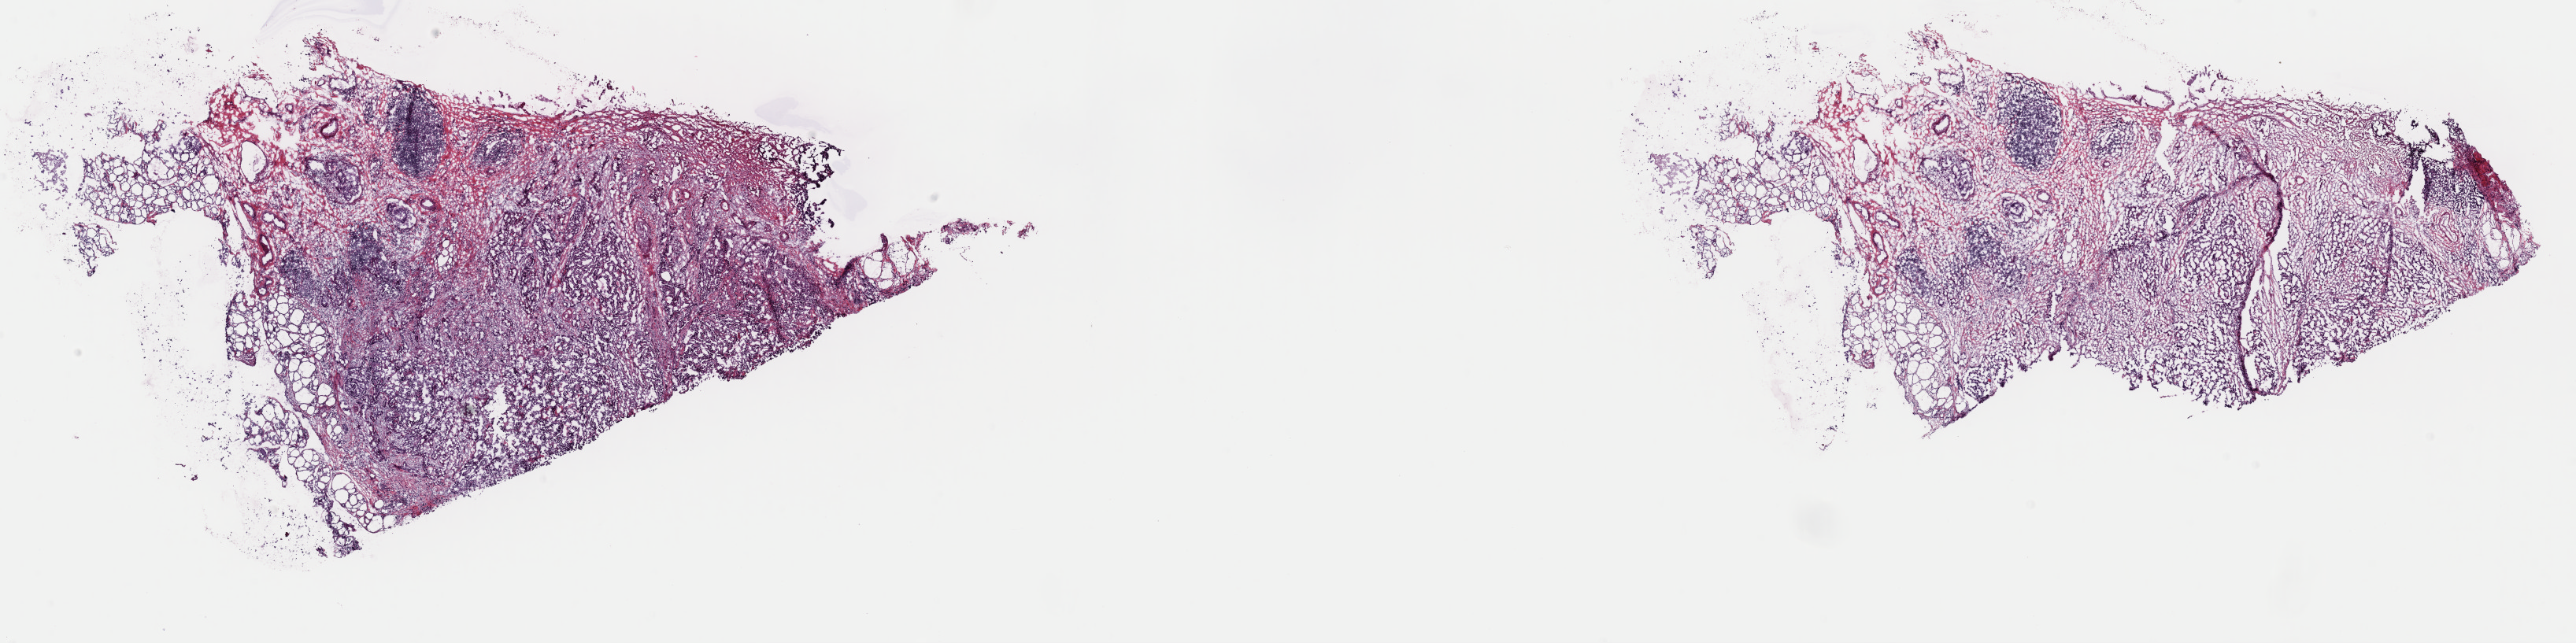
H&E whole-slide image — low-resolution overview of the scanned area, about 25.8 x 6.5 mm (acquisition: 40x scan), frozen section, primary tumour sample from the thyroid. Female patient; age at initial diagnosis 51 years. Composition of this section per pathologist review: tumour cells 65%, tumour nuclei 65%, normal cells 2%, stromal cells 33%, necrosis 0%. Inflammatory infiltration, as recorded: lymphocyte infiltration 10%, monocyte infiltration 1%, neutrophil infiltration 2%.
TNM: T1b N0 M0. AJCC pathologic stage: I (7th edition). Pathologic diagnosis: Papillary adenocarcinoma, NOS (thyroid gland).